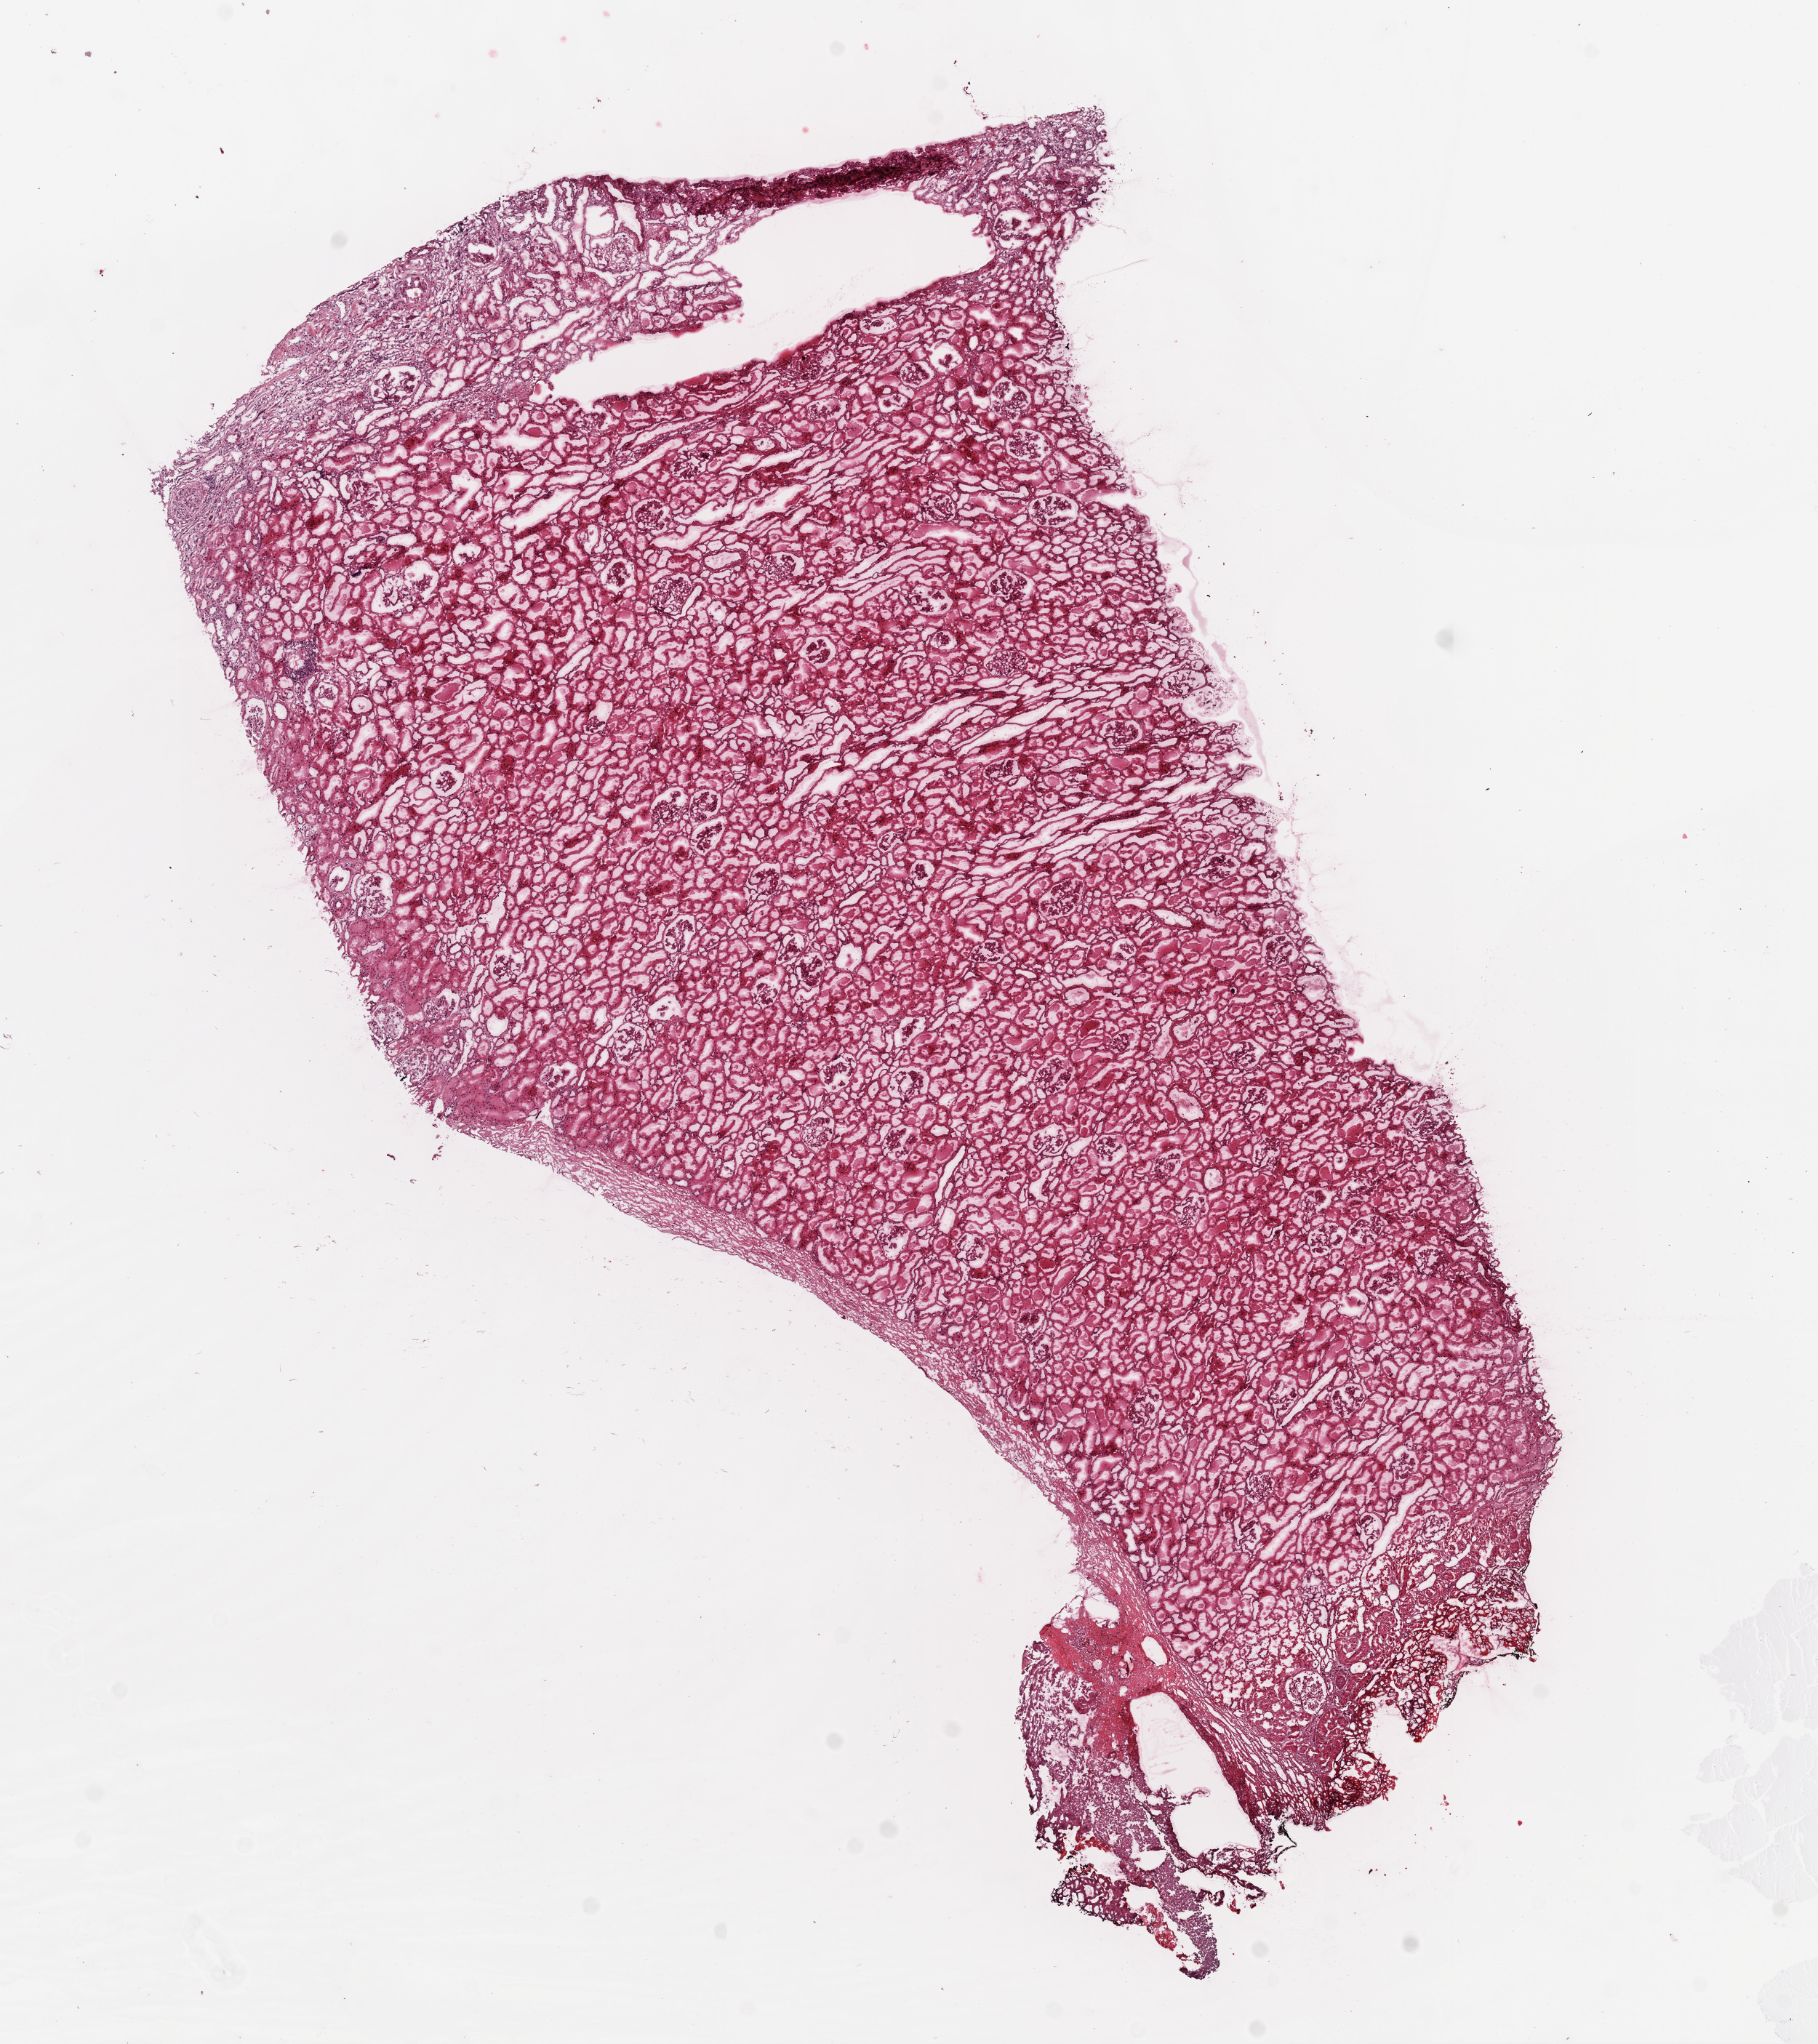
Hematoxylin and eosin (H&E) stained whole-slide image — shown as a low-resolution overview of the whole scanned area (about 10.0 x 11.3 mm), frozen section from the top of the tissue portion, kidney, solid tissue normal (non-tumour tissue) sample. Male, age 40 years at initial diagnosis.
* this section: solid tissue normal sample (biorepository sample class)
* patient diagnosis: Clear cell adenocarcinoma, NOS